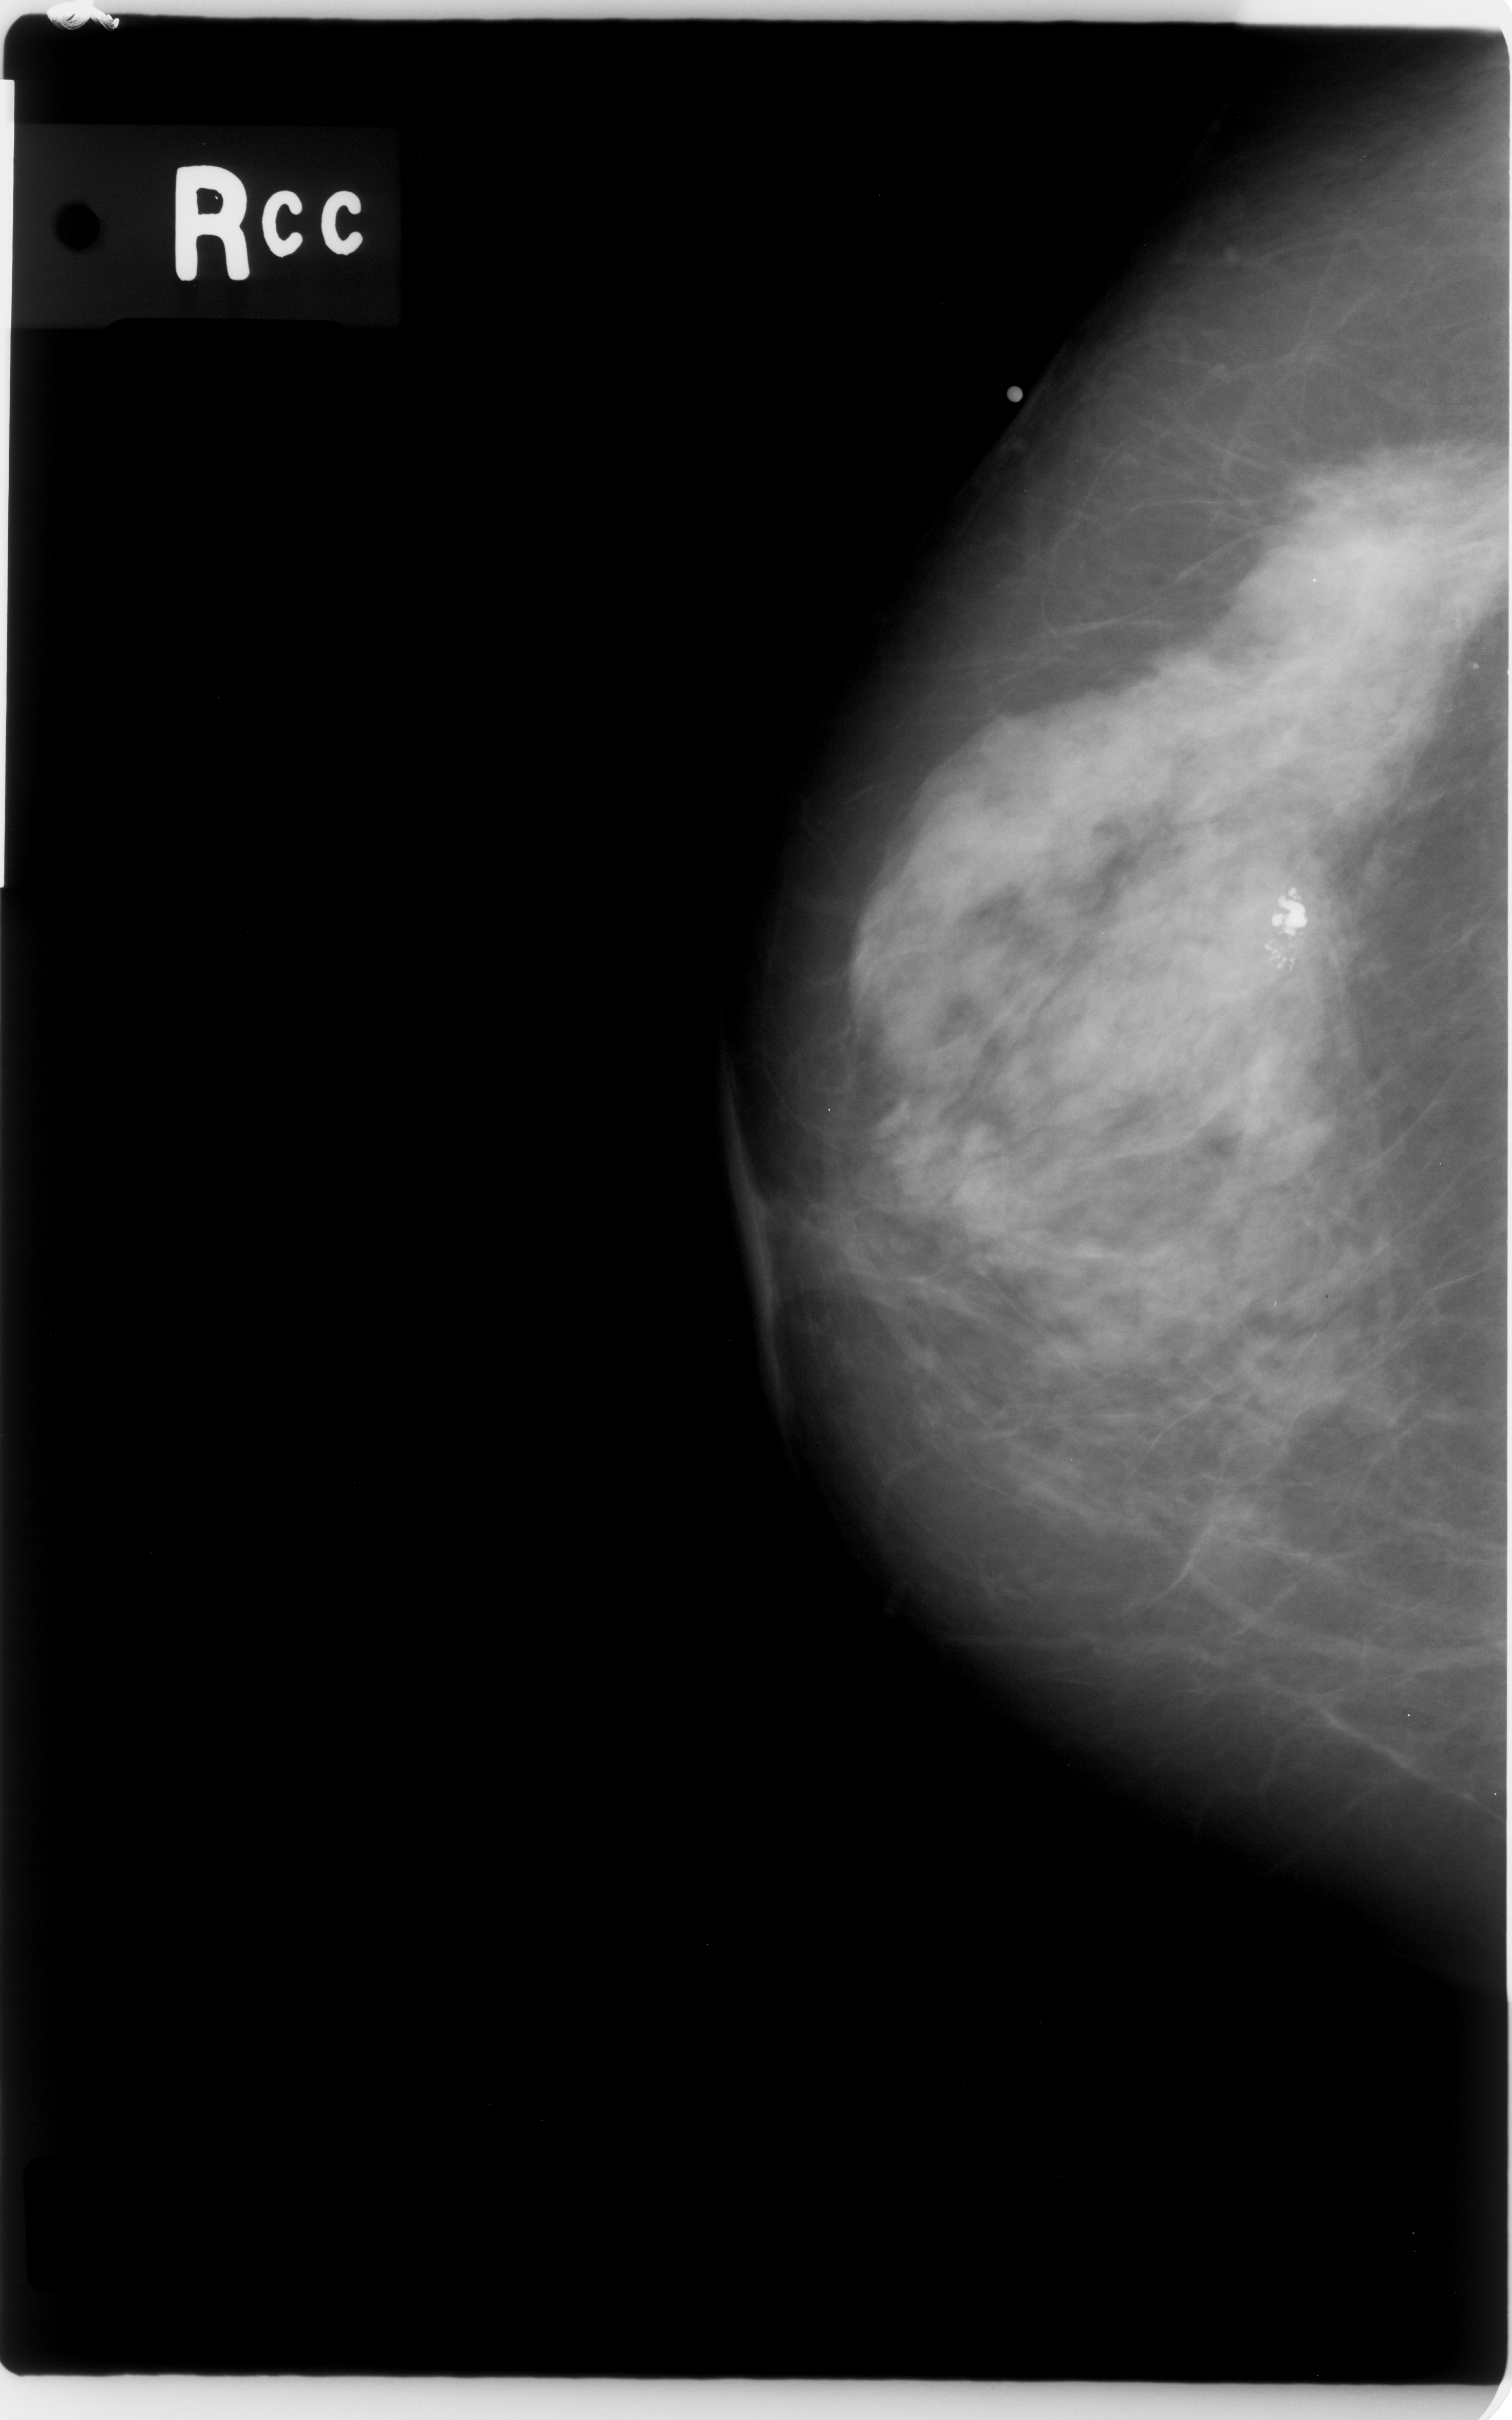
Scanned film-screen mammogram; right breast; CC view; BI-RADS breast density category 3 (scale 1–4).
Finding: mass, shape irregular, margins spiculated; BI-RADS assessment category 5; subtlety rating 5 on a 1 (subtle) to 5 (obvious) scale; pathology result (as recorded, not read from the image): malignant.